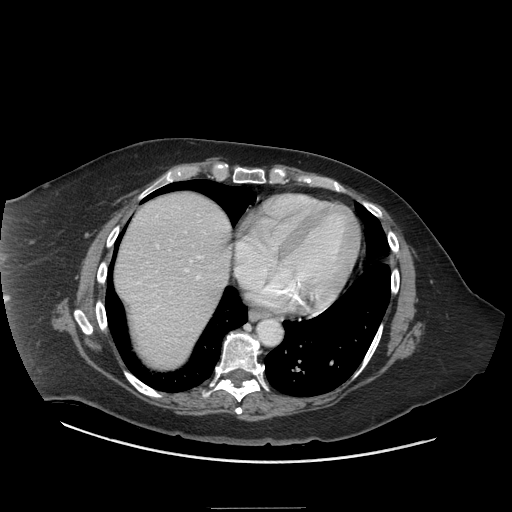
Contrast-enhanced abdominal CT (liver protocol), one axial slice; 140 kVp; soft-tissue window (W 400 / L 40 HU); 2.5 mm slice thickness; 512 × 512 image matrix. From the clinical record (not read from this slice): diagnosis: hepatocellular carcinoma (patient treated with transarterial chemoembolisation; whether this scan precedes or follows treatment is not stated here); TNM stage (as recorded): Stage-II; Child-Pugh class: A.
Structures marked on this image (semi-automatically segmented with operator editing):
- abdominal aorta: bounding box [x1, y1, x2, y2] px = [258, 319, 281, 346]
- liver parenchyma outside the tumour (the mass and vessels are separate outlines, so this box may not span the whole liver): [114, 193, 230, 368]
- liver vessels: [122, 207, 227, 341]